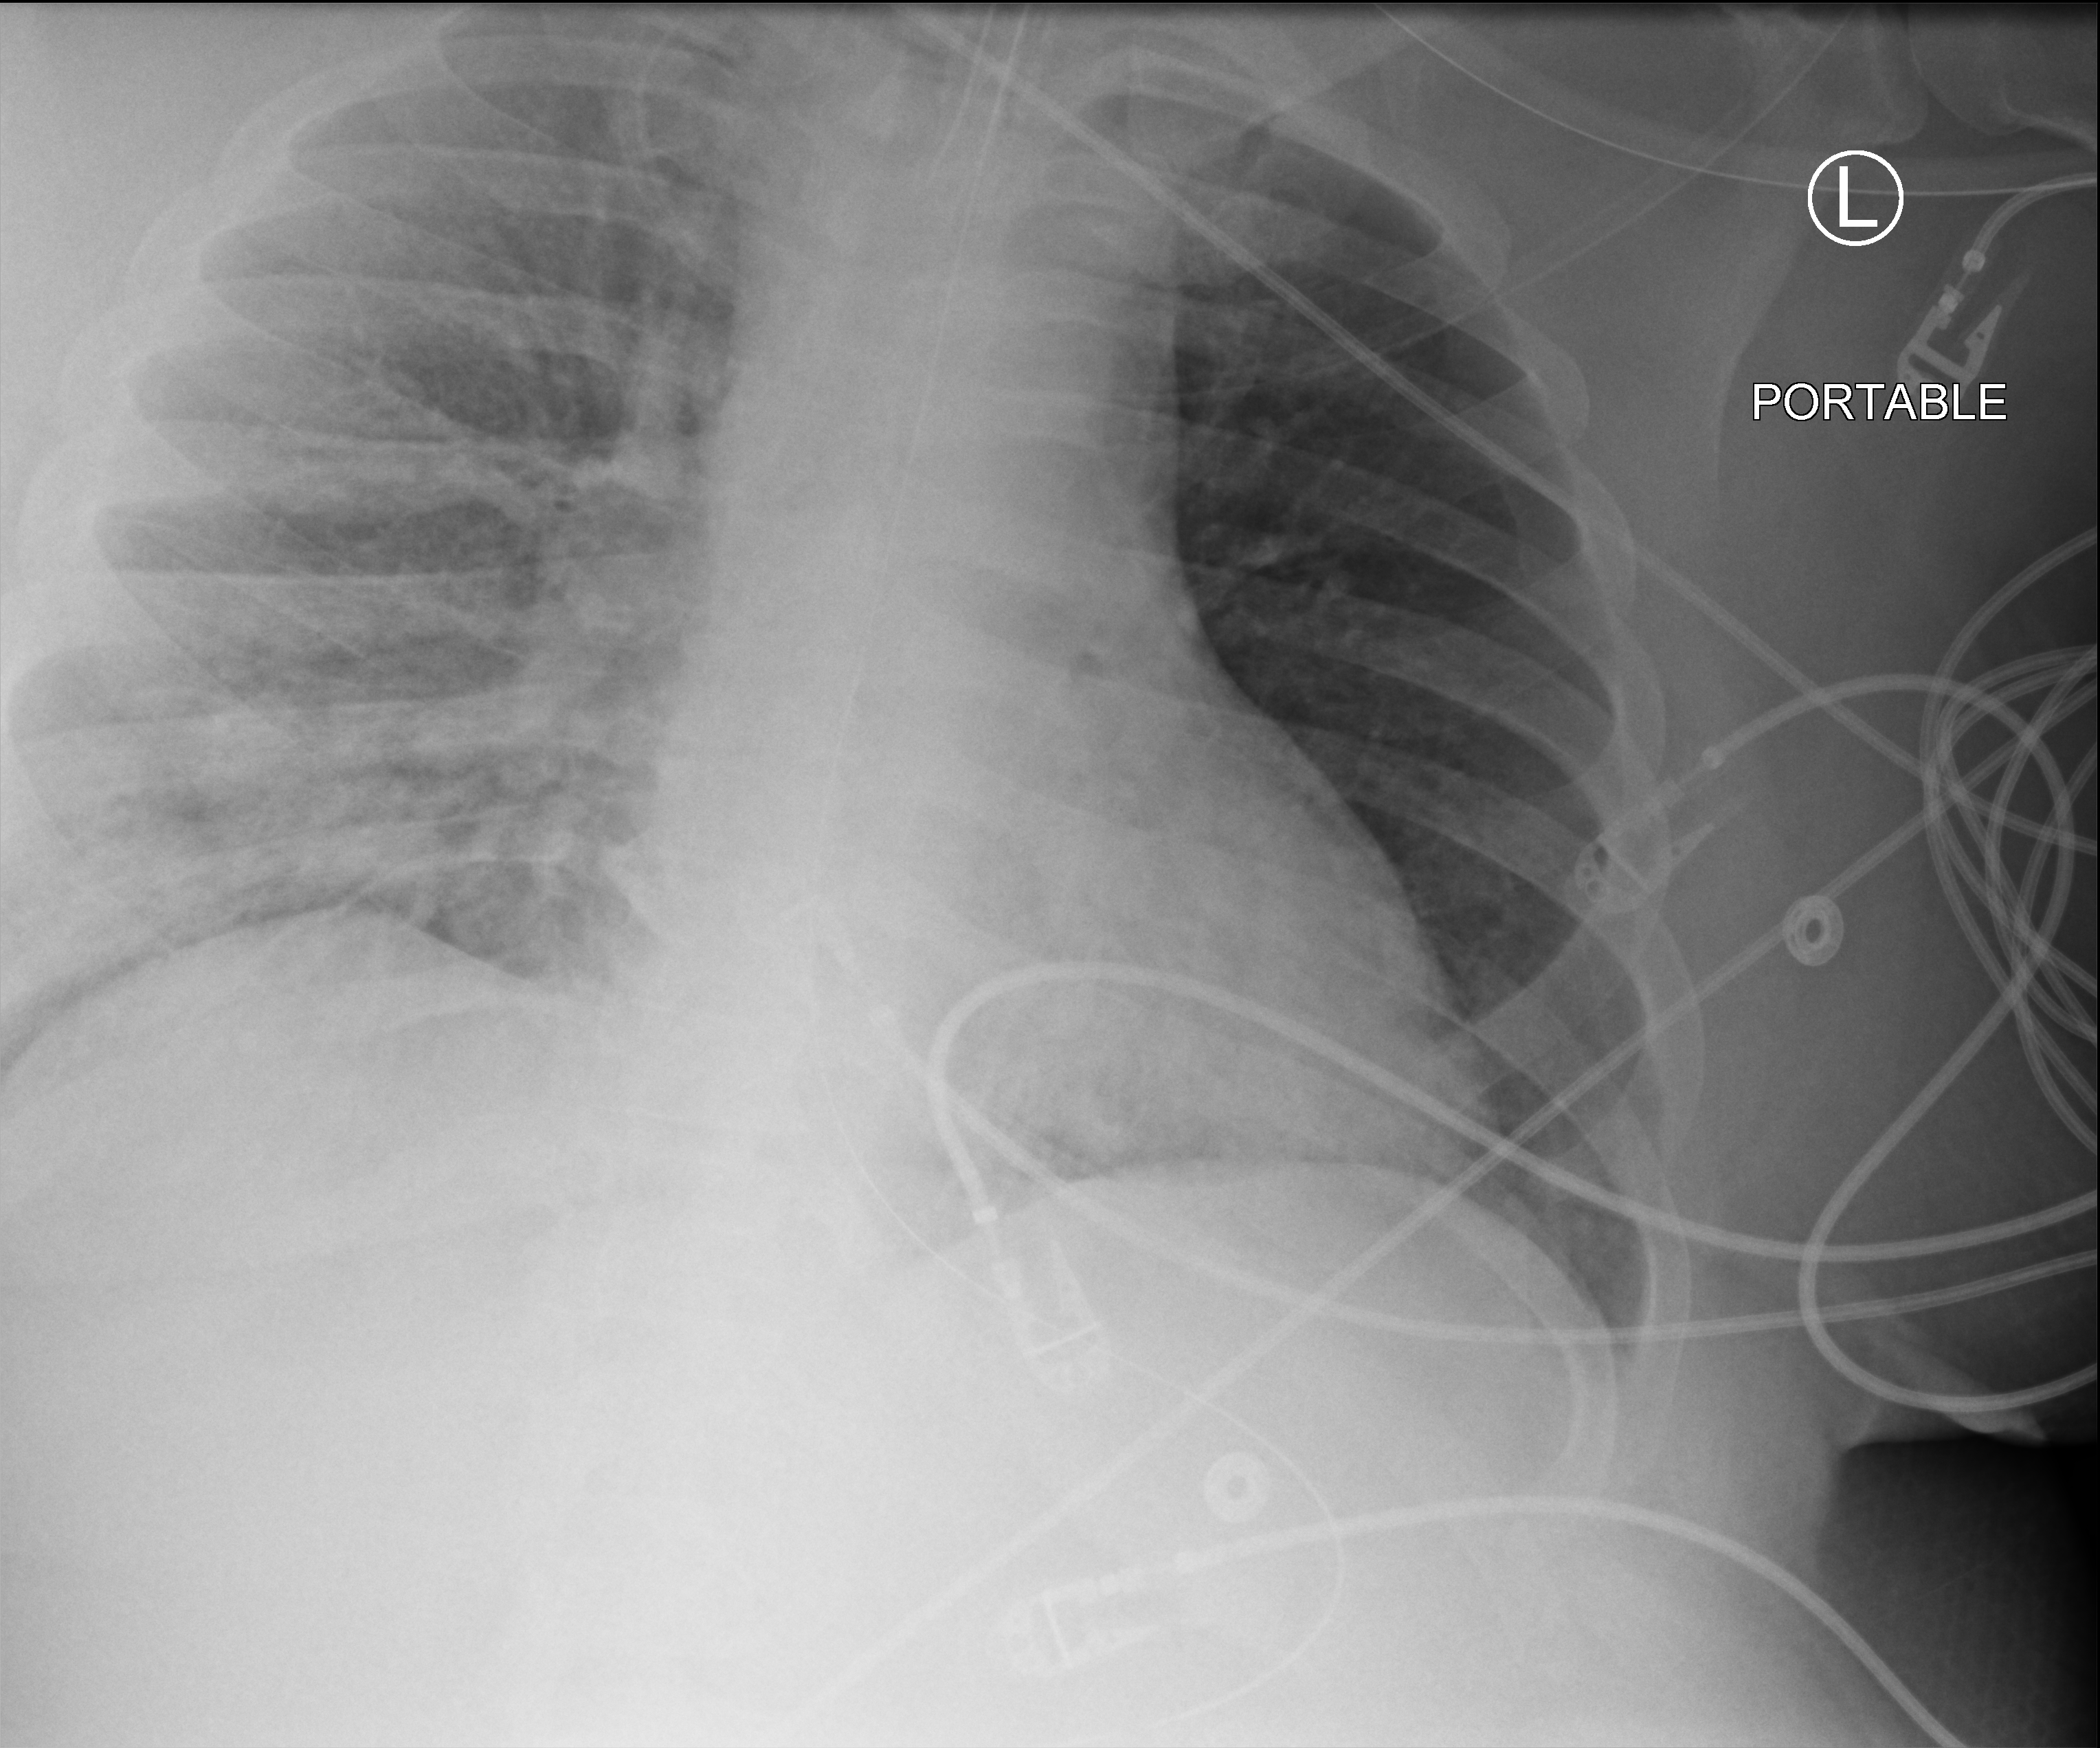
Chest X-ray (portable), anteroposterior (AP) projection. Patient hospitalised with COVID-19, aged 18–59 years.
Hospital-stay facts (about this admission, not read from this image; timing relative to this image not recorded):
- mechanically ventilated during this hospital stay: yes
- length of hospital stay: 10 days
- diabetes (admission record): yes